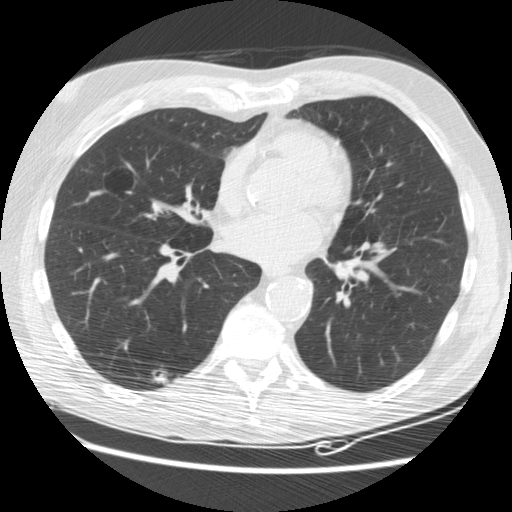
Low-dose screening chest CT, axial slice; third annual screen; lung window (W 1500 / L -600 HU); 2.5 mm slice thickness; slice 97 of 176 in the series. Male, age 62 years at enrolment. Current smoker at enrolment.
Expert-annotated lung lesion, bounding box <142,360,179,396> (left, top, right, bottom; pixels). The screening reader recorded 3 non-calcified nodules or masses ≥4 mm on this exam (right lower lobe, right lower lobe, right lower lobe); which of them this box marks is not recorded. Official screen result: positive, other. Lung cancer was diagnosed 33 days after this screen: adenocarcinoma, NOS, right lower lobe, moderately differentiated (G2), stage IIIB (AJCC 6th edition), 15 mm at pathology.